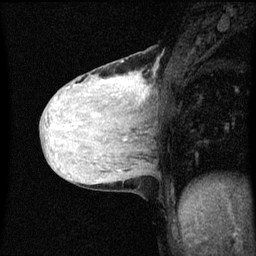
Breast MRI (dynamic contrast-enhanced), one sagittal slice. Position 25 of 60 along the scan axis. Dynamic contrast-enhanced series, image 2 of 3 at this slice position (ordered by acquisition). 1.5 T. TE 4.2 ms, TR 8.4 ms. 2 mm slice thickness. 256 × 256 image matrix, field of view 200 × 200 mm. Female patient, age 36 years.
Outlined on this slice (semi-automatically segmented with operator editing):
- analysis volume of interest (the breast-tissue region the enhancement analysis was run in; not a lesion): bounding box [x1, y1, x2, y2] px = [48, 52, 159, 151]
- tumour enhancement mask (voxels above the 70 % enhancement threshold inside the analysis volume of interest): [142, 92, 147, 99]